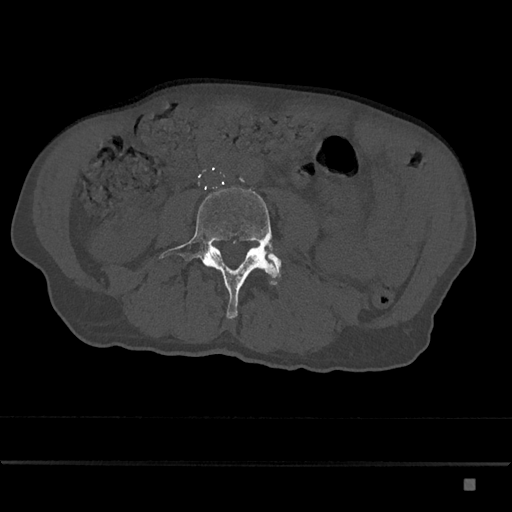
CT including the spine, one axial slice. Slice 340 of 797 in the series (ordered by position). Bone window (W 1800 / L 400 HU). 0.5 mm slice thickness. 512 × 512 image matrix. Patient: male, 72 years. Case-level facts recorded for this patient, not image findings: primary cancer: prostate.
Outlined on this slice (semi-automatic segmentation, software-assisted and operator-edited):
- L4 vertebra: bounding box <159,186,281,319> (left, top, right, bottom; pixels)
- L5 vertebra: <270,255,281,271>